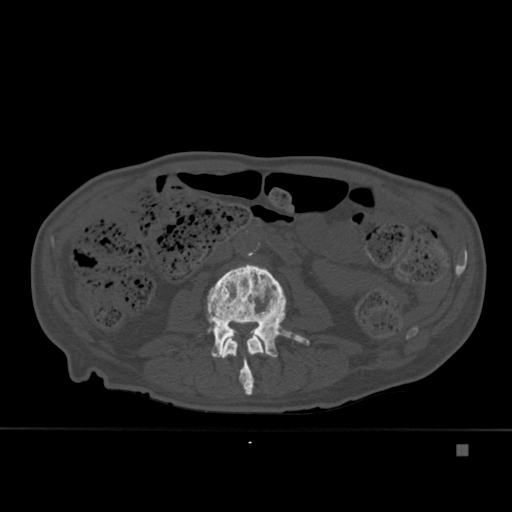
CT including the spine, one axial slice. Slice 148 of 451 in the series (ordered by position). Bone window (W 1800 / L 400 HU). 512 × 512 image matrix. Patient: male, 75 years. Case-level facts recorded for this patient, not image findings: primary cancer: prostate.
Annotated regions visible in this slice (semi-automatically segmented with operator editing):
- L2 vertebra: bounding box <222,335,265,395> (left, top, right, bottom; pixels)
- L3 vertebra: <207,264,310,376>